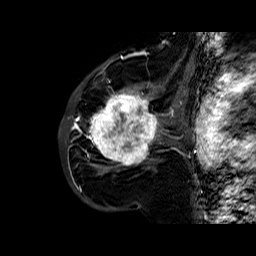
Breast MRI (dynamic contrast-enhanced), one sagittal slice; slice 39 of 60 in the series (ordered by position); dynamic contrast-enhanced series, time point 2 of 6 at this slice position (early post-contrast); 1.5 T; TE 6.4 ms, TR 32.8 ms; 256 × 256 image matrix, field of view 200 × 200 mm. Female patient. From the clinical record (not read from this slice): setting: breast cancer imaged before/during neoadjuvant chemotherapy; receptor status: HR-positive, HER2-negative.
Structures marked on this image (semi-automatic segmentation, software-assisted and operator-edited):
- analysis volume of interest (the breast-tissue region the enhancement analysis was run in; not a lesion): bounding box <86,77,163,177> (left, top, right, bottom; pixels)
- tumour enhancement mask (voxels above the 100 % enhancement threshold inside the analysis volume of interest): <88,82,159,166>